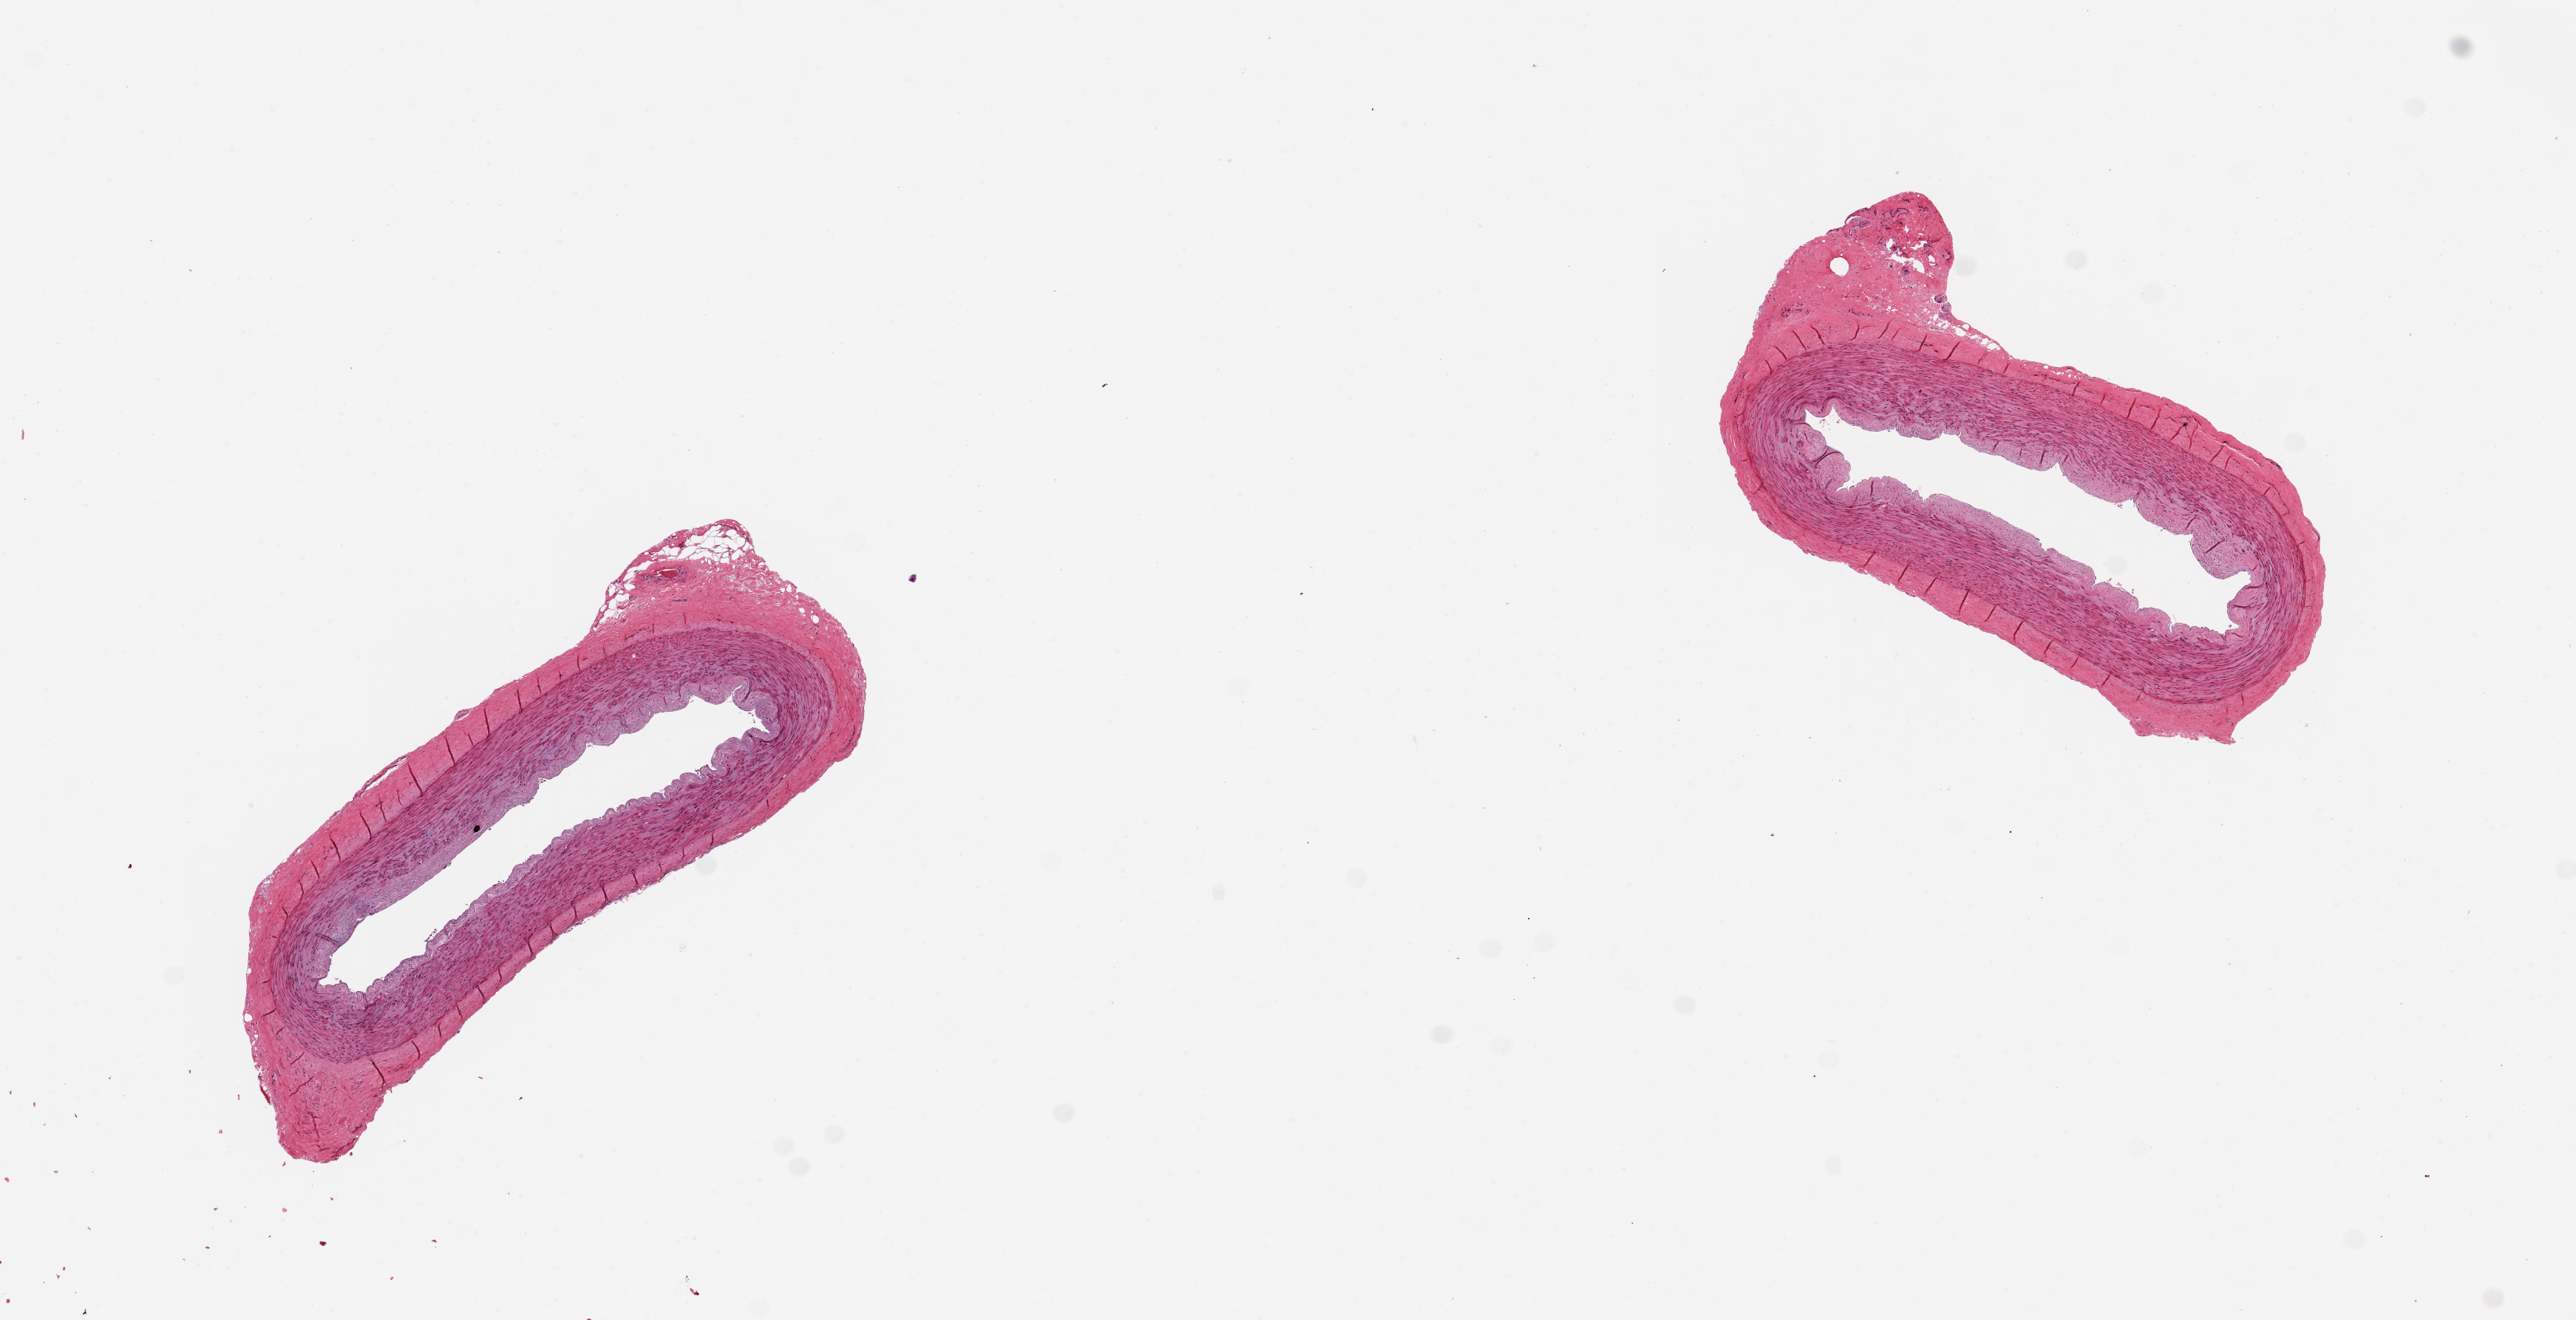
Digitized hematoxylin and eosin (H&E)-stained section, shown as a low-resolution overview of the whole scanned area (about 13.8 x 7.1 mm, from a 20x scan), PAXgene-fixed paraffin-embedded (PFPE) section, sampled site (target tissue): tibial artery, tissue donor sample.
Reviewer comment on this tissue sample: 2 pieces ~2mm d. Clean specimens.